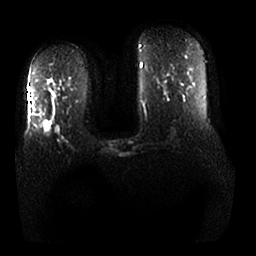
Breast MRI, one axial slice; slice 14 of 25 in the series (ordered by position); diffusion-weighted series; image 2 of 4 stored at this slice position (different b-values; order by instance number); 1.5 T; 4 mm slice thickness; 256 × 256 image matrix, field of view 380 × 380 mm. Female patient.
Annotated regions visible in this slice (manually delineated by an expert):
- tumour on diffusion-weighted imaging: bounding box (x1, y1, x2, y2) in pixels: (43, 121, 51, 133)